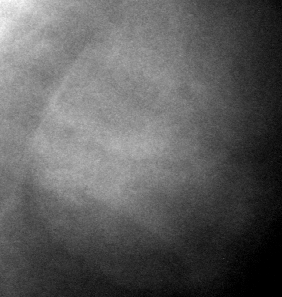
Crop from a digitized film mammogram around one marked abnormality, left breast, MLO view, BI-RADS breast density category 3 (scale 1–4).
Marked abnormality: mass, shape oval, margins circumscribed; BI-RADS assessment category 4; pathology result (as recorded, not read from the image): benign.